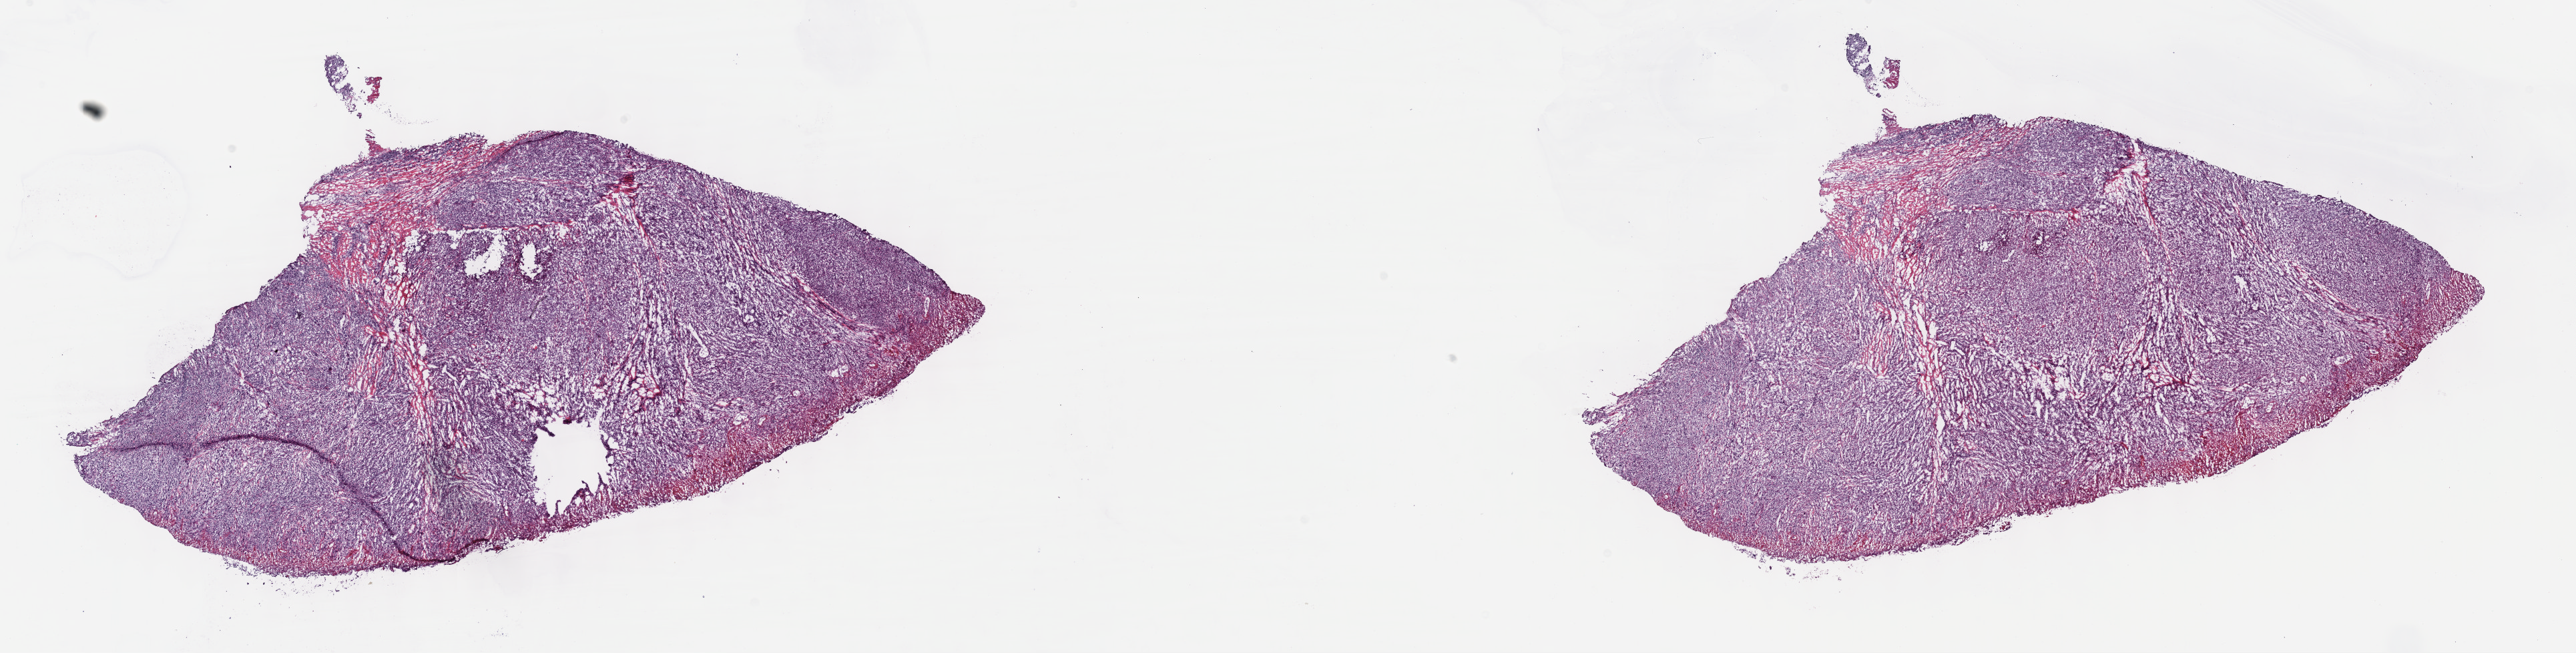
Hematoxylin and eosin (H&E) stained whole-slide image — whole scanned area (about 31.2 x 7.9 mm, acquisition: 40x scan) shown as a low-resolution overview, frozen section from the top of the tissue portion, primary tumour sample from the skin. Patient: female, age at initial diagnosis 58 years. Composition of this section per pathologist review: tumour cells 100%, tumour nuclei 80%, normal cells 0%, stromal cells 0%, necrosis 0%. Infiltration values recorded for this section: lymphocyte infiltration 3%, monocyte infiltration 0%, neutrophil infiltration 0%.
Pathologic diagnosis: Malignant melanoma, NOS.